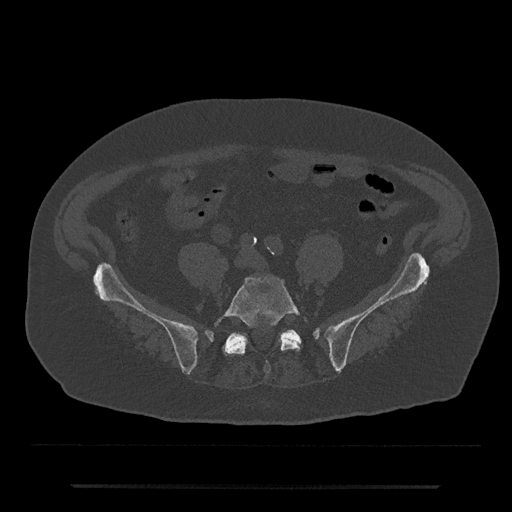
CT including the spine, one axial slice. Slice 276 of 797 in the series (ordered by position). Reconstruction kernel Br40s/3. 120 kVp. Bone window (W 1800 / L 400 HU). 0.5 mm slice thickness. 512 × 512 image matrix, field of view 434 × 434 mm. Patient: male, 80 years. From the clinical record (not read from this slice): primary cancer: prostate; vertebrae with lytic lesions (as recorded): L1, T11.
Outlined on this slice (semi-automatic segmentation, software-assisted and operator-edited):
- L5 vertebra: bounding box <214,276,301,373> (left, top, right, bottom; pixels)